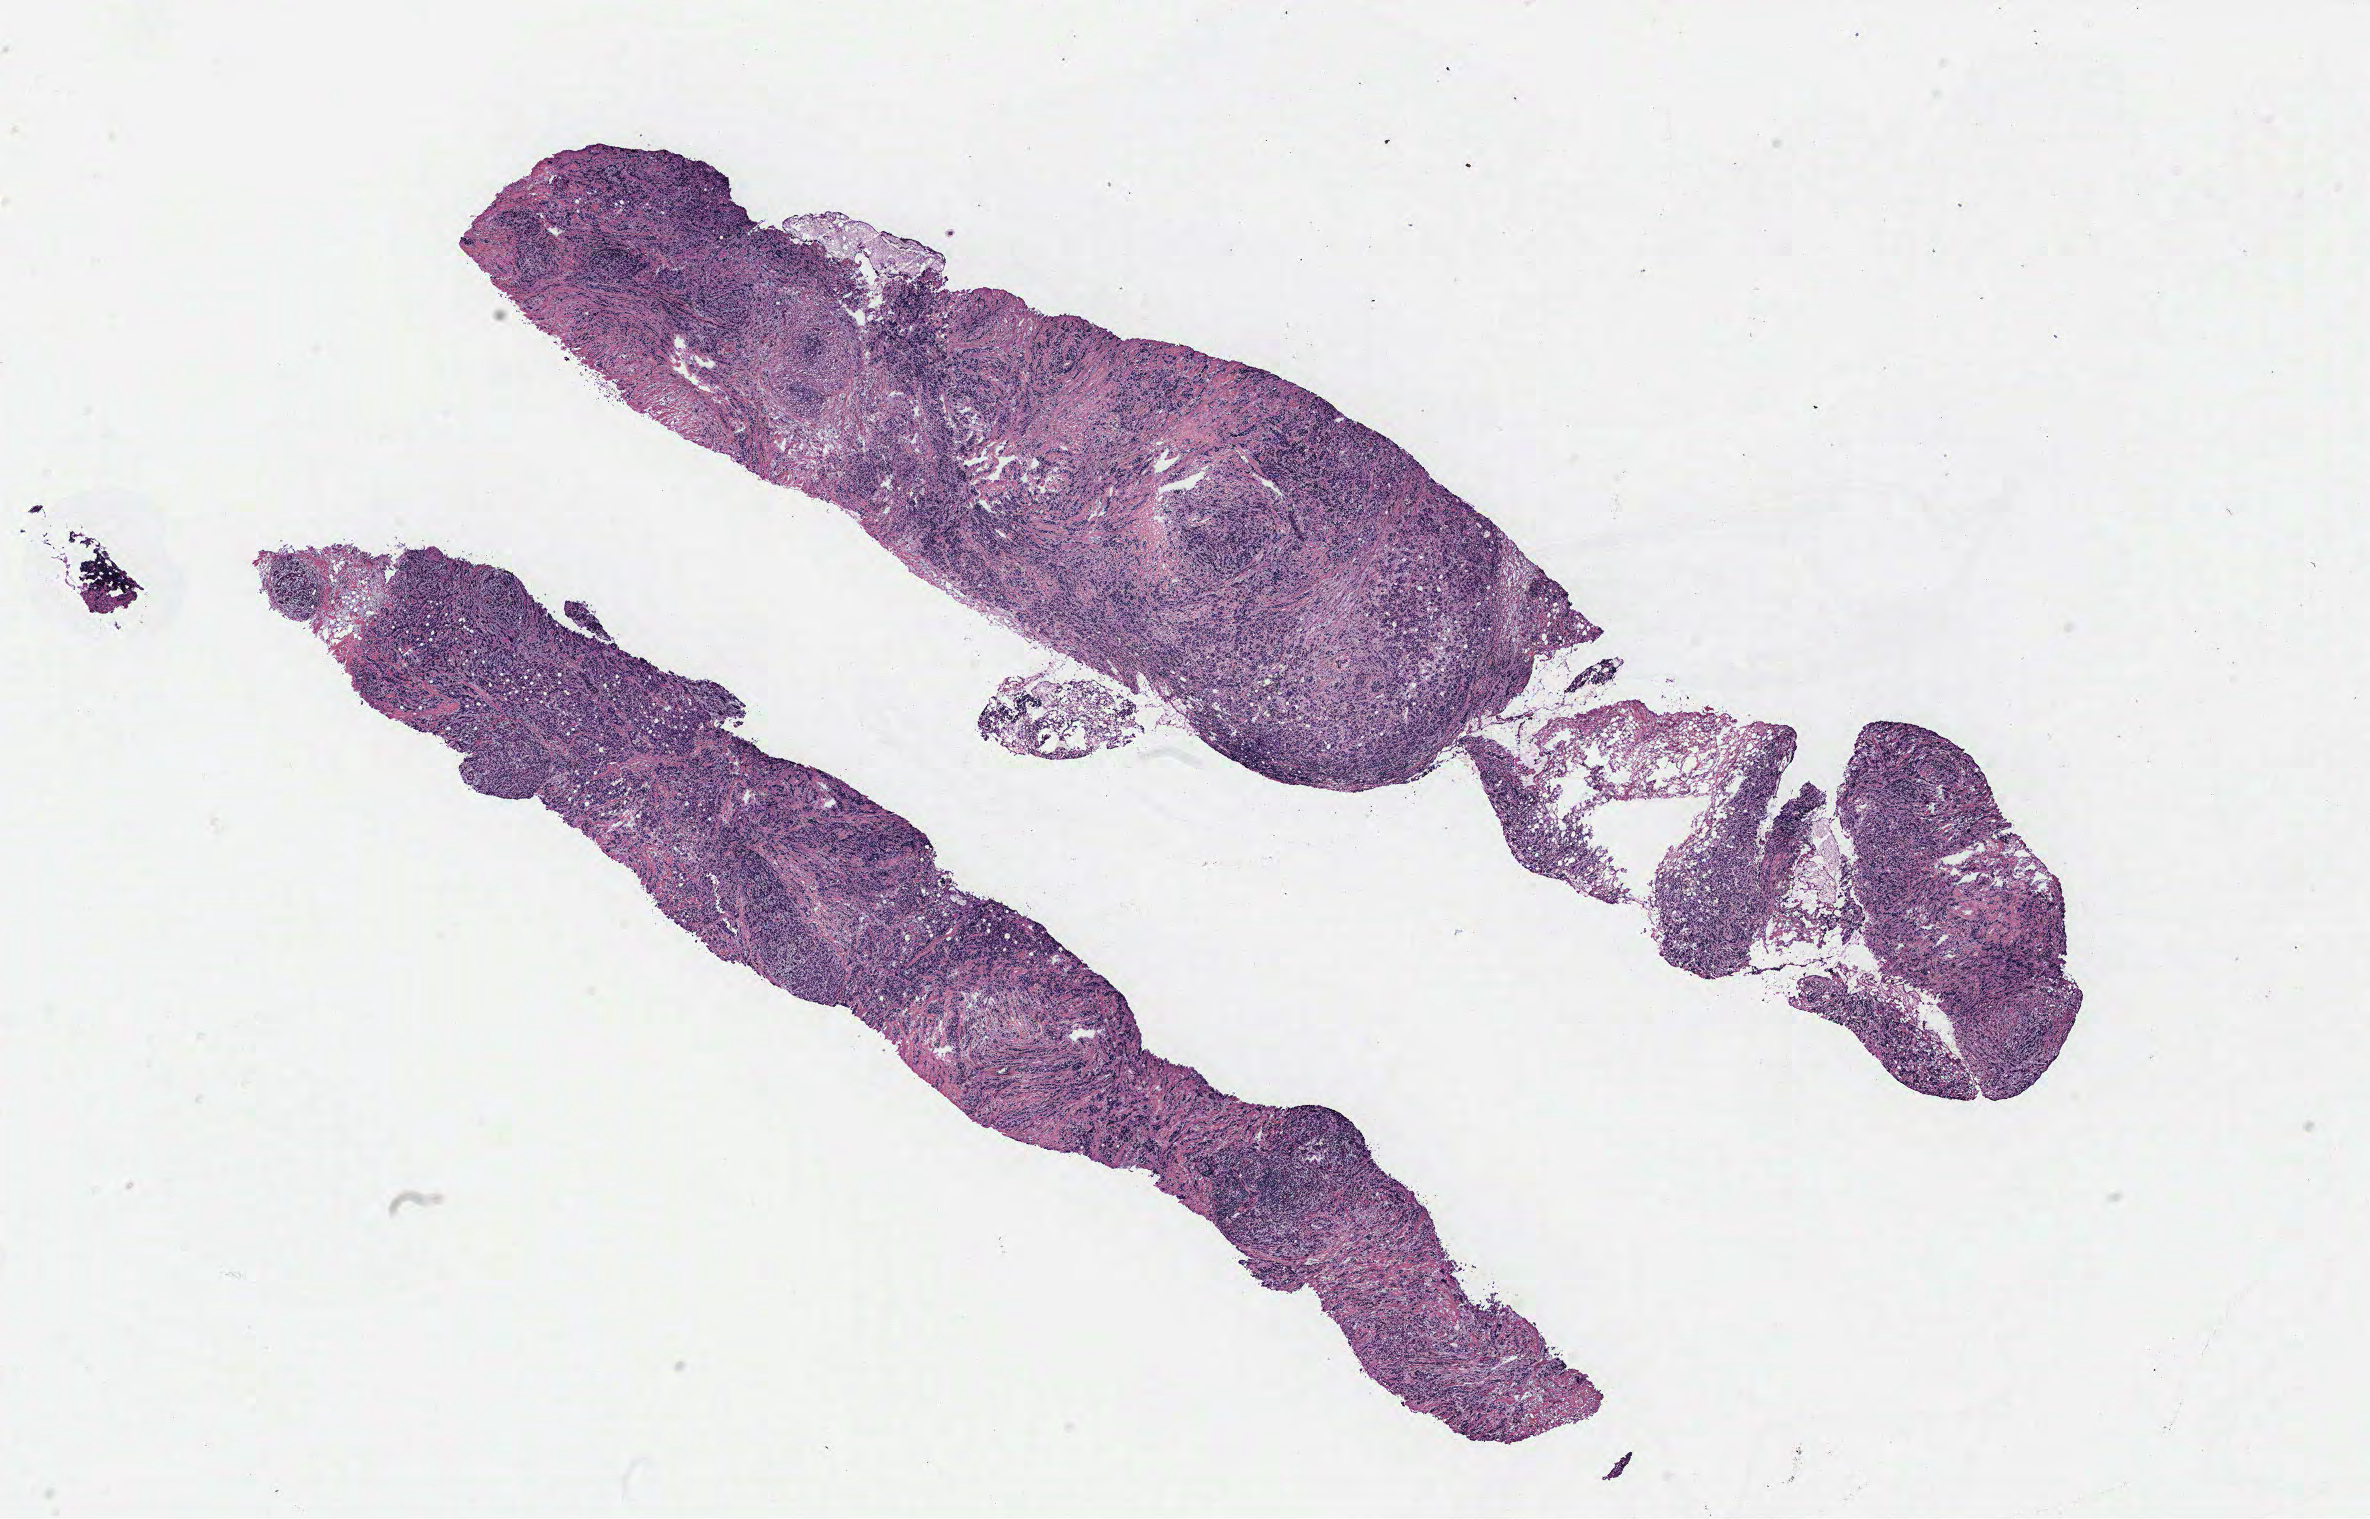
Digitized H&E tissue section (whole slide) — a low-resolution overview of the entire scanned area, about 19.0 x 12.2 mm. Breast, tissue type not recorded.
Patient diagnosis (cohort enrolment): breast cancer (breast).